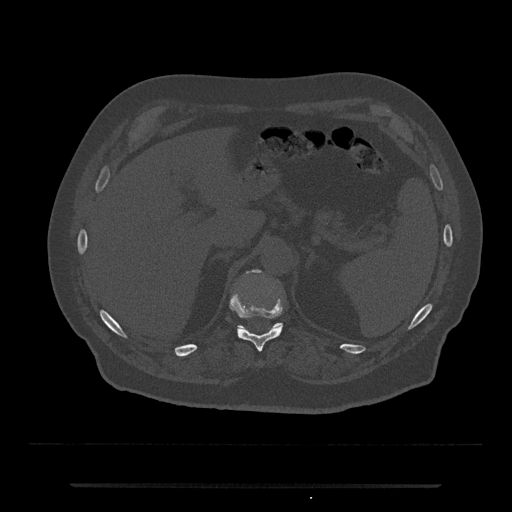
CT including the spine, one axial slice. Position 638 of 797 along the scan axis. Reconstruction kernel Br40s/3. 120 kVp. Bone window (W 1800 / L 400 HU). 0.5 mm slice thickness. 512 × 512 image matrix, field of view 434 × 434 mm. Male patient, age 80 years. Case-level facts recorded for this patient, not image findings: primary cancer: prostate.
Outlined on this slice (semi-automatic segmentation, software-assisted and operator-edited):
- T11 vertebra: bounding box [x1, y1, x2, y2] px = [230, 294, 283, 352]
- T12 vertebra: [236, 269, 283, 331]